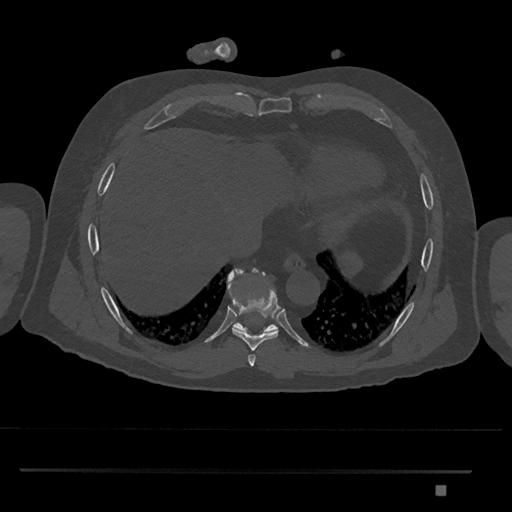
CT including the spine, one axial slice. Slice 1092 of 1134 in the series (ordered by position). Bone window (W 1800 / L 400 HU). 0.5 mm slice thickness. 512 × 512 image matrix, field of view 429 × 429 mm. Patient: male, 65 years. From the clinical record (not read from this slice): primary cancer: prostate.
Structures marked on this image (semi-automatically segmented with operator editing):
- T8 vertebra: bounding box [x1, y1, x2, y2] px = [232, 269, 280, 350]
- T9 vertebra: [227, 268, 278, 333]